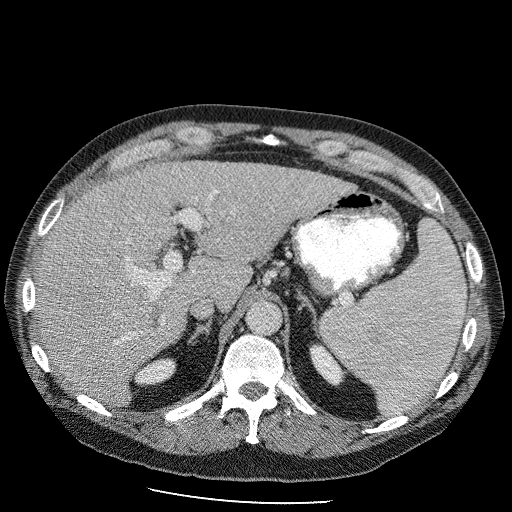
Contrast-enhanced abdominal CT (liver protocol), one axial slice; slice 67 of 98 in the series (ordered by position); reconstruction kernel STANDARD; soft-tissue window (W 400 / L 40 HU); 2.5 mm slice thickness; 512 × 512 image matrix, field of view 400 × 400 mm. Case-level facts recorded for this patient, not image findings: diagnosis: hepatocellular carcinoma (patient treated with transarterial chemoembolisation; whether this scan precedes or follows treatment is not stated here); TNM stage (as recorded): Stage-II; Child-Pugh class: B; tumour differentiation: moderately differentiated.
Outlined on this slice (semi-automatic segmentation, software-assisted and operator-edited):
- liver parenchyma outside the tumour (the mass and vessels are separate outlines, so this box may not span the whole liver): bounding box (x1, y1, x2, y2) in pixels: (36, 160, 356, 404)
- liver vessels: (112, 249, 201, 342)